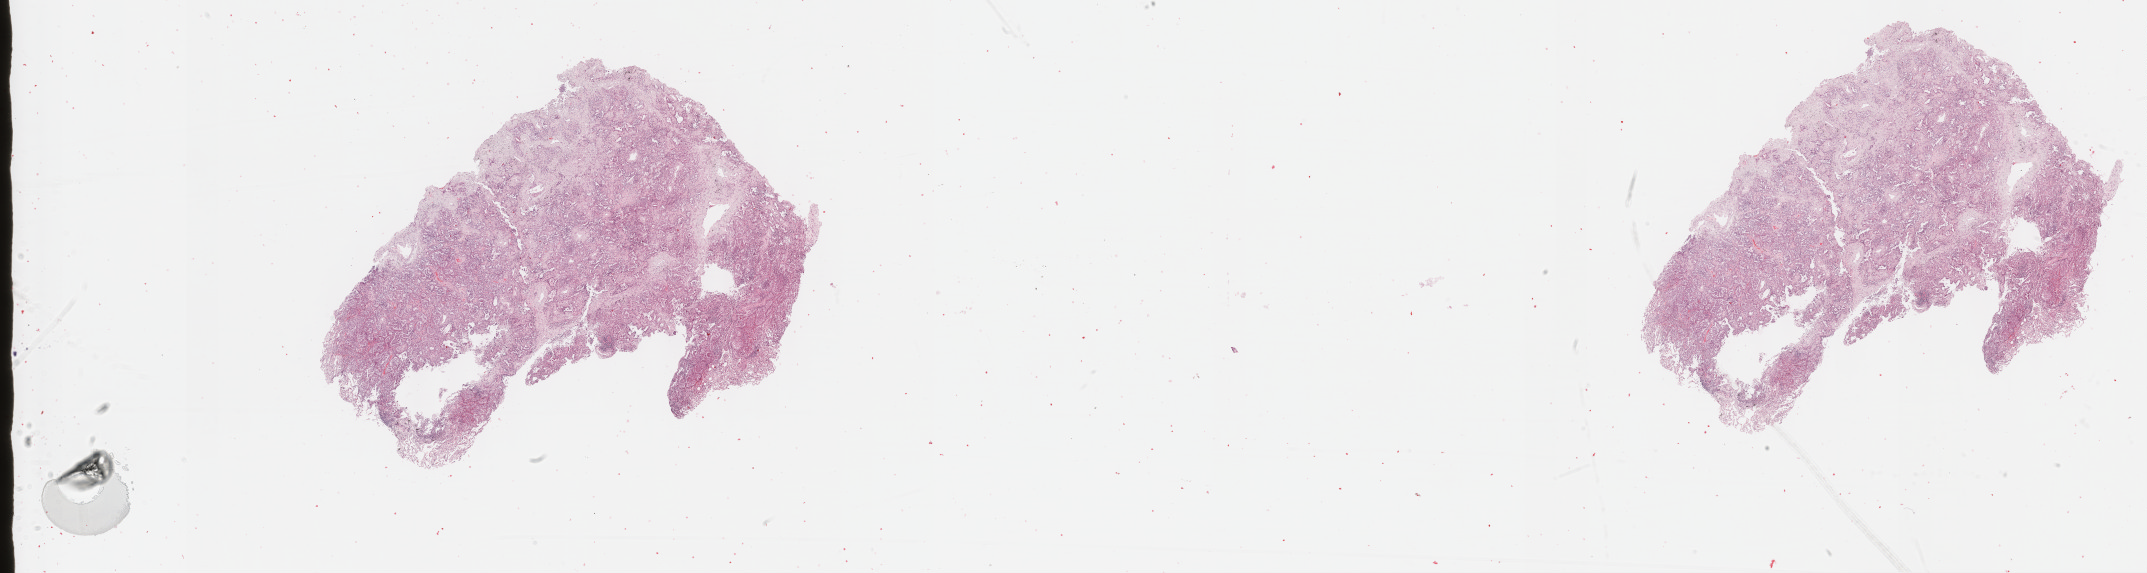
Whole-slide histology image, H&E — shown as a low-resolution overview of the whole scanned area (about 34.7 x 9.3 mm); FFPE section; sample: primary tumour, lung. Patient: female, age at initial diagnosis 84 years.
- AJCC pathologic stage: IB (6th edition)
- diagnosis: Adenocarcinoma, NOS (lower lobe, lung)